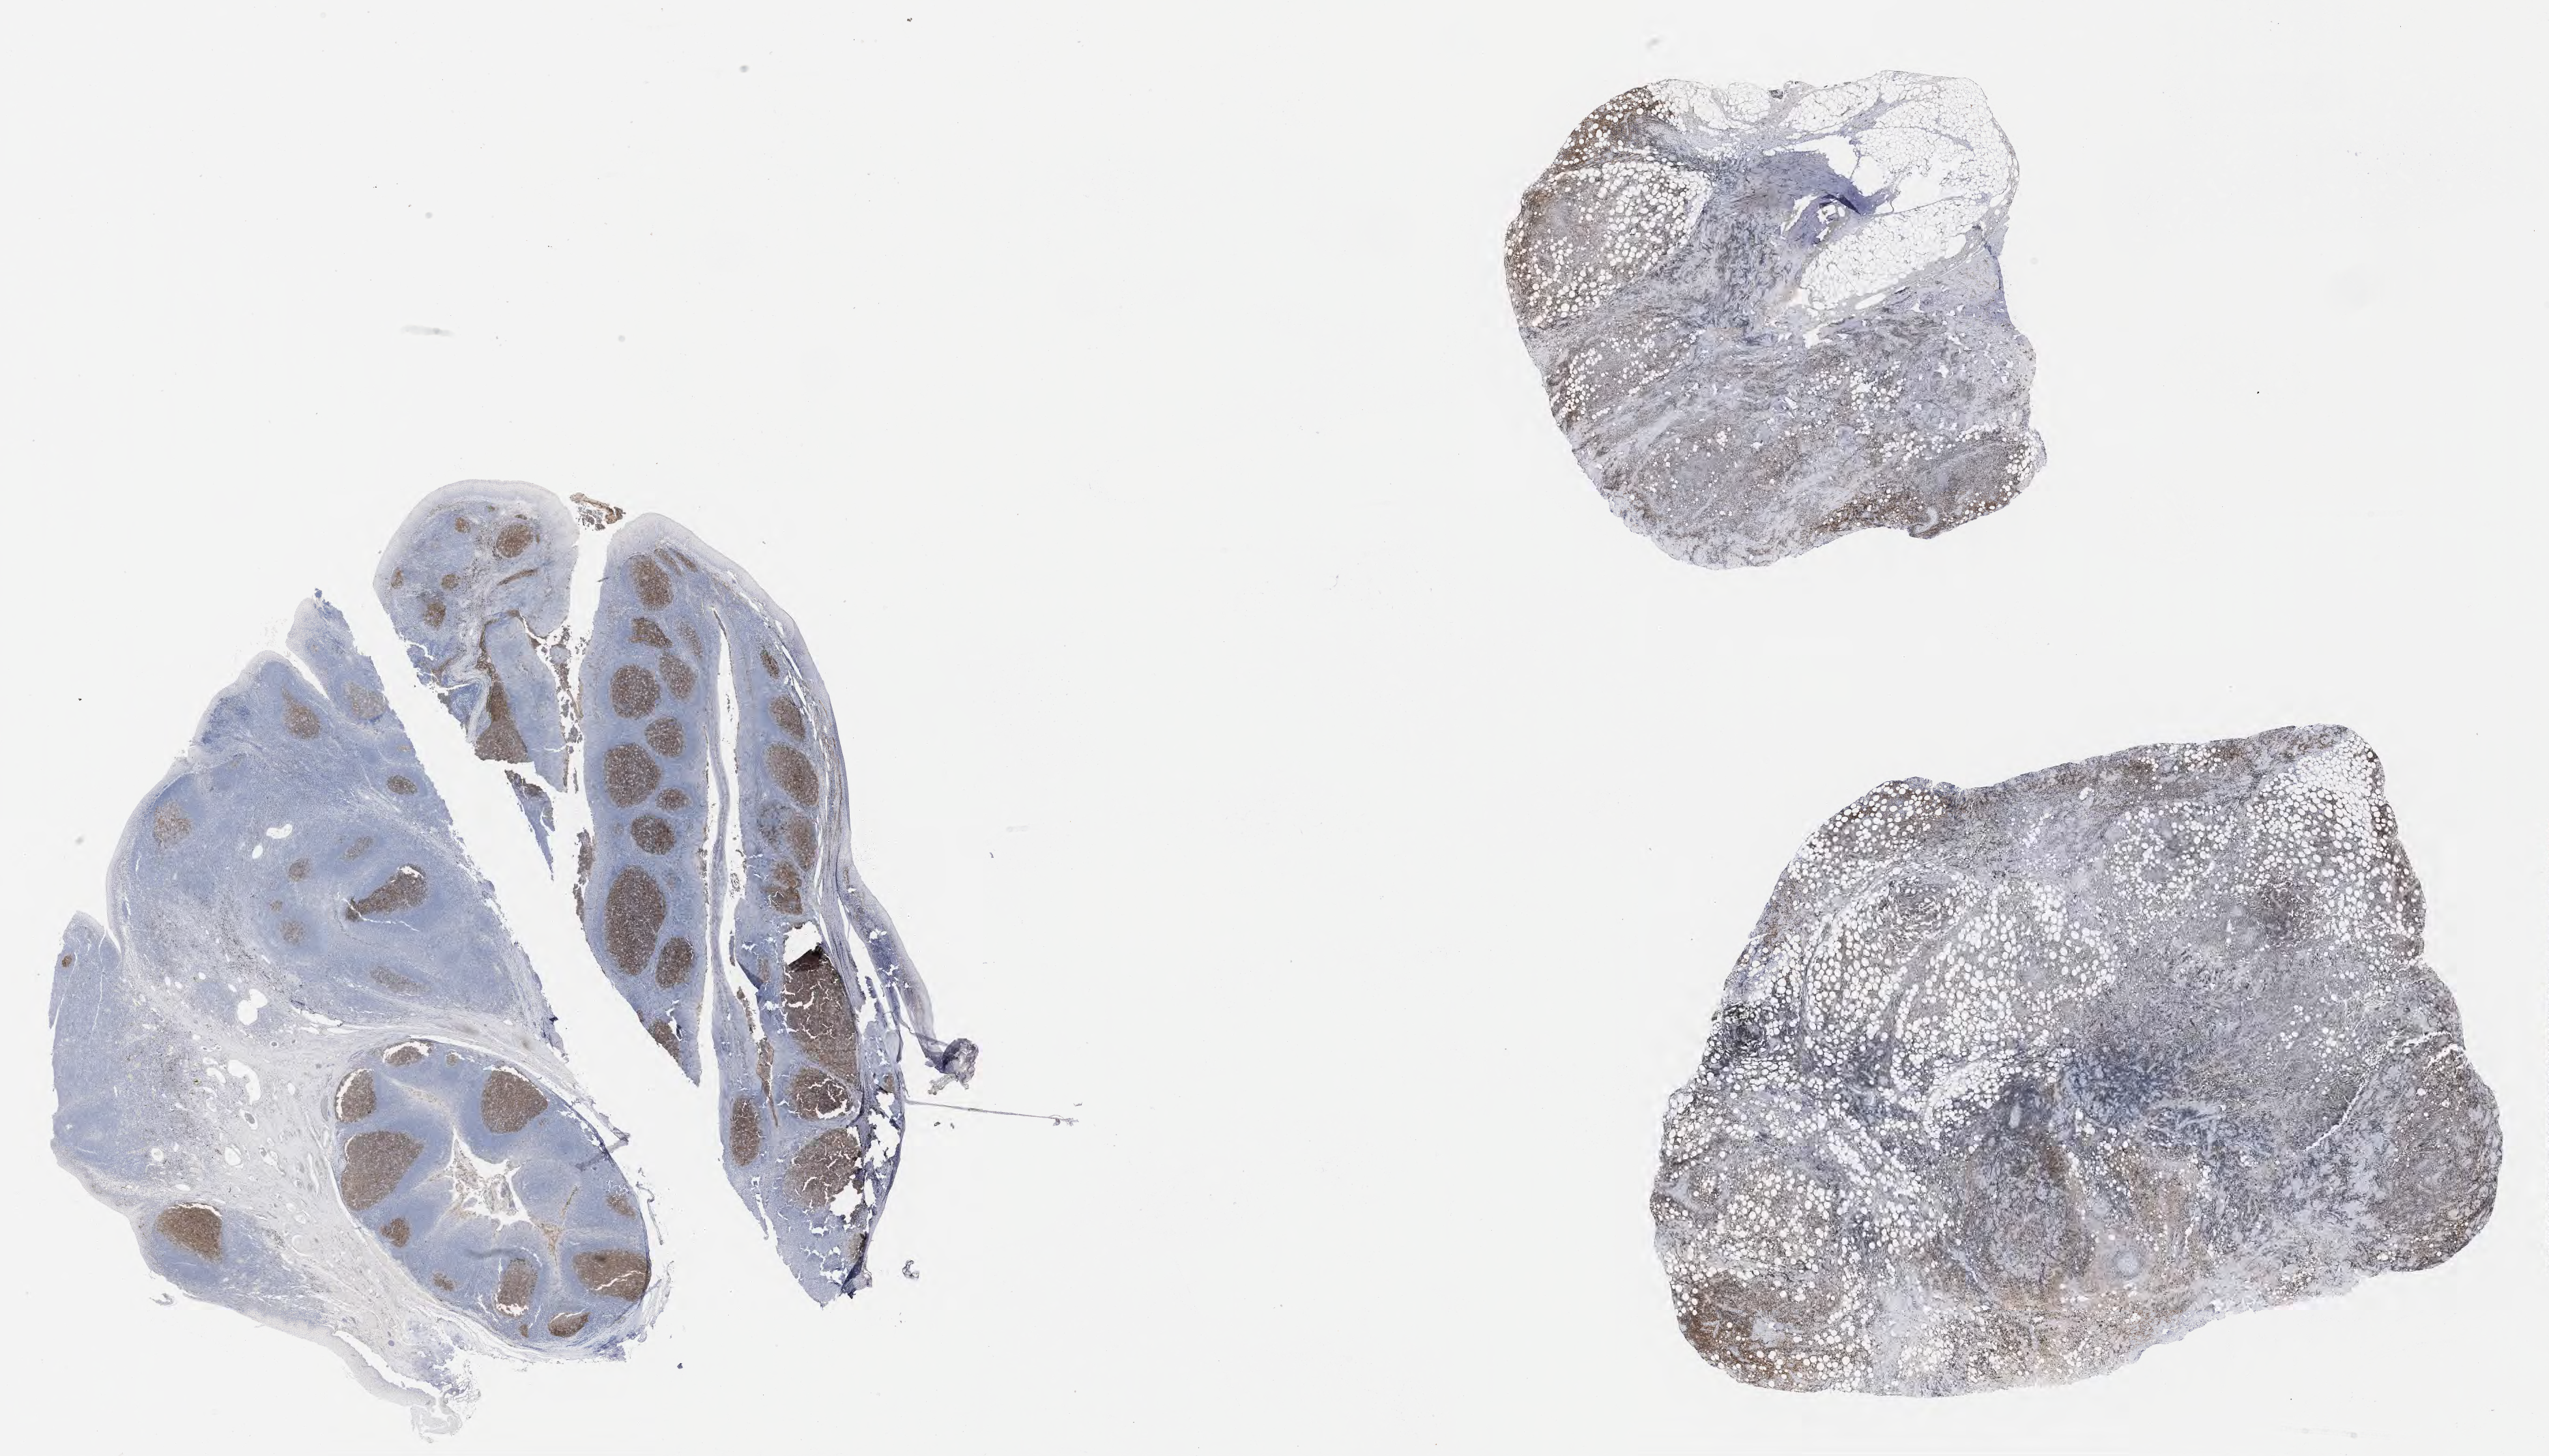
Immunohistochemistry (IHC) whole-slide image stained for CD10, whole scanned area (about 30.2 x 17.2 mm) shown as a low-resolution overview; tumor tissue; anatomic site: kidney. Male patient, aged 63.
* histologic diagnosis: Diffuse large B-cell lymphoma, NOS